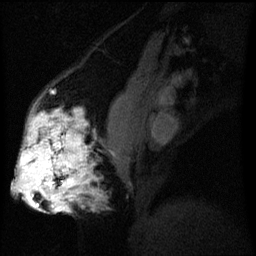
Breast MRI (dynamic contrast-enhanced), one sagittal slice. Position 24 of 60 along the scan axis. Dynamic contrast-enhanced series, image 2 of 3 at this slice position (ordered by acquisition). 1.5 T. TE 4.2 ms, TR 8 ms. 2.2 mm slice thickness. 256 × 256 image matrix, field of view 200 × 200 mm. Patient: female, 50 years.
Annotated regions visible in this slice (semi-automatic segmentation, software-assisted and operator-edited):
- analysis volume of interest (the breast-tissue region the enhancement analysis was run in; not a lesion): bounding box [x1, y1, x2, y2] px = [19, 112, 95, 211]
- tumour enhancement mask (voxels above the 70 % enhancement threshold inside the analysis volume of interest): [19, 114, 87, 211]